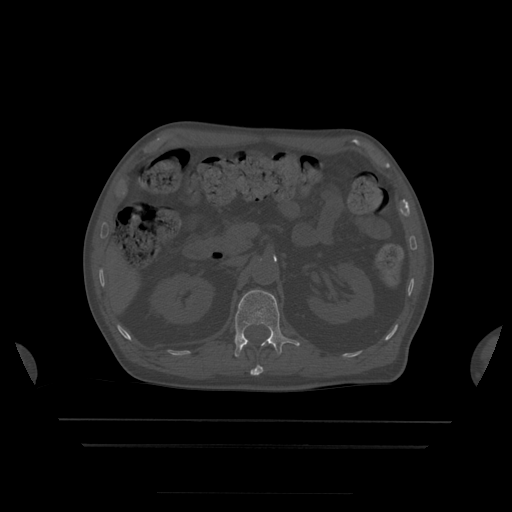
CT including the spine, one axial slice. Slice 176 of 522 in the series (ordered by position). Bone window (W 1800 / L 400 HU). 512 × 512 image matrix, field of view 436 × 436 mm. Patient age 68 years. From the clinical record (not read from this slice): primary cancer: urothelial.
Annotated regions visible in this slice (semi-automatically segmented with operator editing):
- L1 vertebra: bounding box <235,290,301,357> (left, top, right, bottom; pixels)
- T12 vertebra: <251,365,264,376>